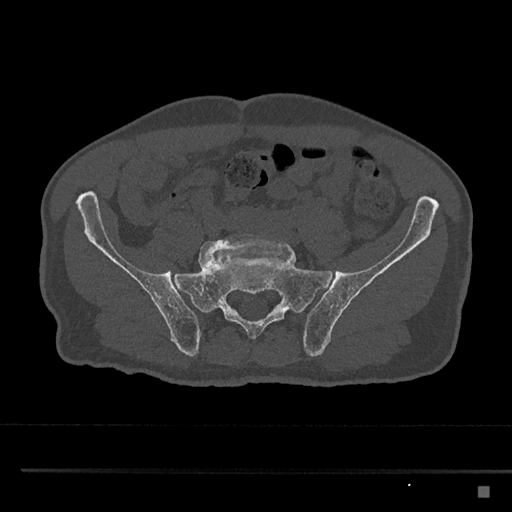
CT including the spine, one axial slice. Position 536 of 797 along the scan axis. Bone window (W 1800 / L 400 HU). 0.5 mm slice thickness. 512 × 512 image matrix, field of view 391 × 391 mm. Patient: male, 59 years. Case-level facts recorded for this patient, not image findings: primary cancer: prostate.
Outlined on this slice (semi-automatic segmentation, software-assisted and operator-edited):
- L5 vertebra: bounding box <198,234,290,270> (left, top, right, bottom; pixels)